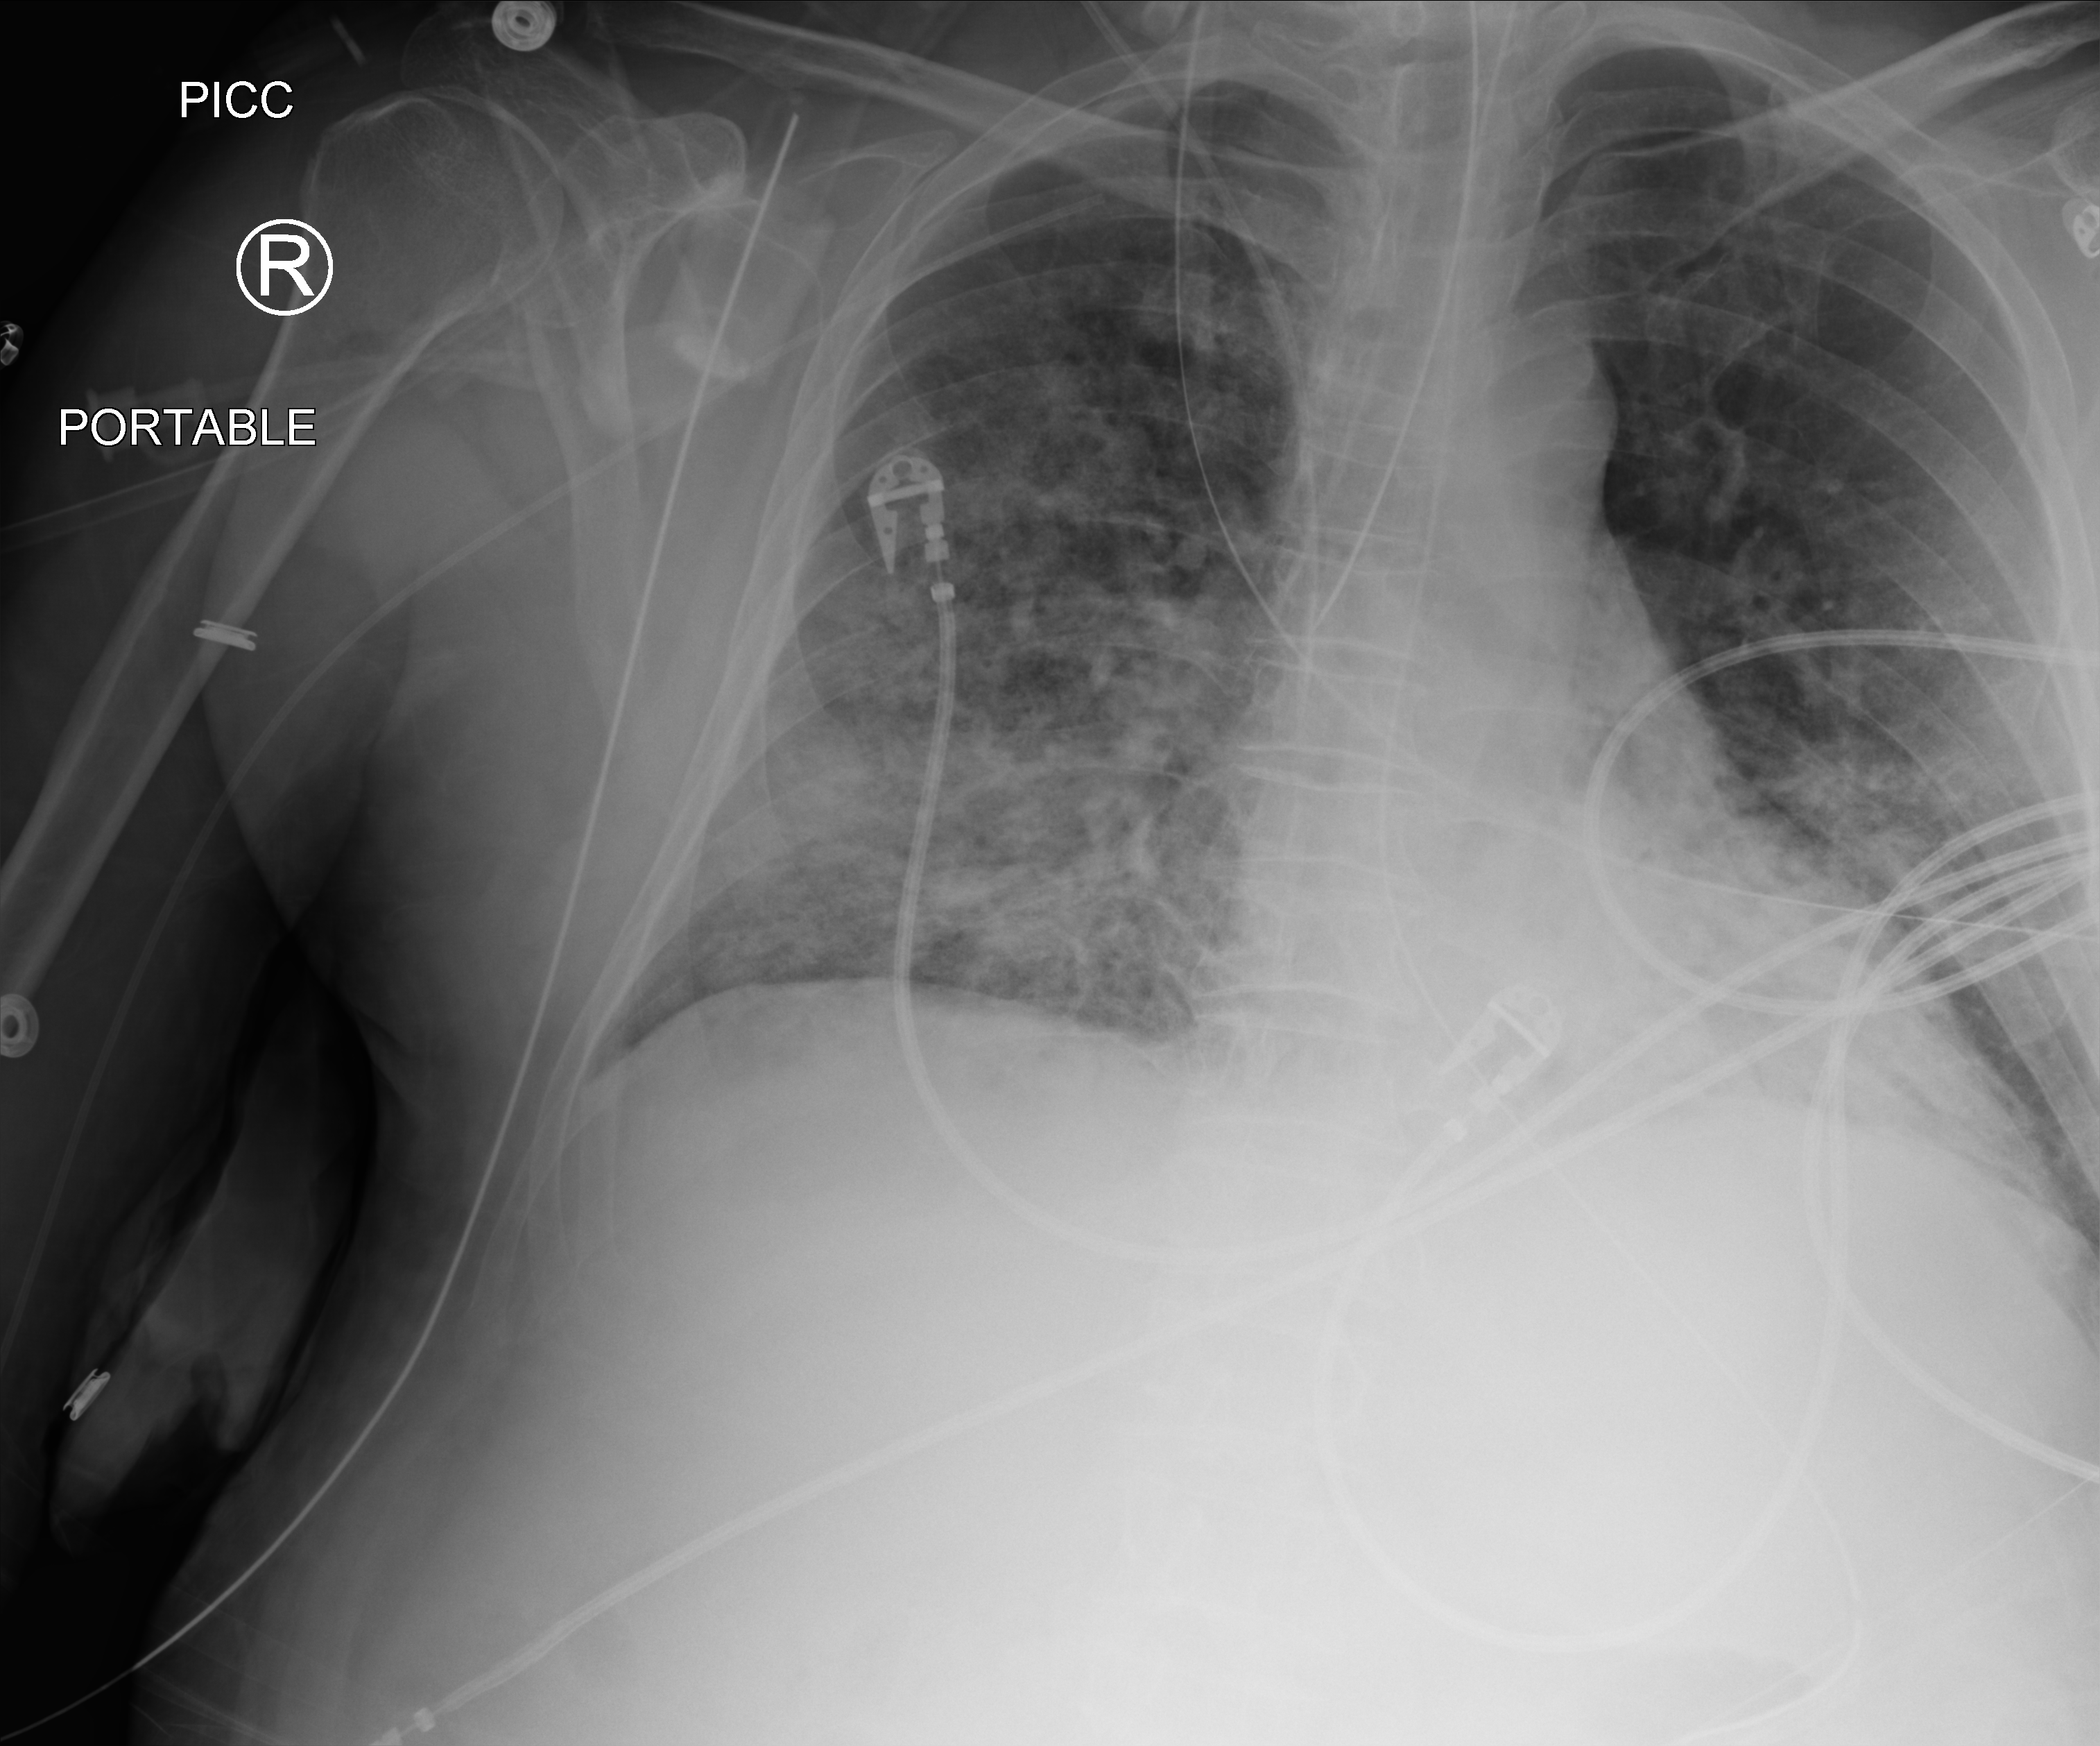
Chest X-ray (portable); anteroposterior (AP) projection. Male patient hospitalised with COVID-19, age 60–74 years.
From the hospital-stay record, not from the radiograph (when in the stay this image was taken is not recorded):
- mechanically ventilated during this hospital stay: yes
- COPD (admission record): no
- admitted to intensive care during this hospital stay: yes